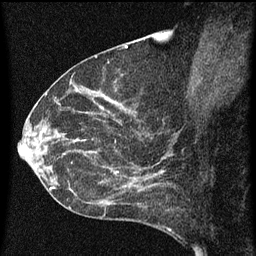
Breast MRI (dynamic contrast-enhanced), one sagittal slice; dynamic contrast-enhanced series, image 2 of 3 at this slice position (ordered by acquisition); 1.5 T; TE 4.2 ms, TR 8 ms; 2 mm slice thickness; 256 × 256 image matrix, field of view 180 × 180 mm. Patient: female, 54 years.
Outlined on this slice (semi-automatically segmented with operator editing):
- analysis volume of interest (the breast-tissue region the enhancement analysis was run in; not a lesion): bounding box <49,138,164,209> (left, top, right, bottom; pixels)
- tumour enhancement mask (voxels above the 70 % enhancement threshold inside the analysis volume of interest): <50,140,161,205>